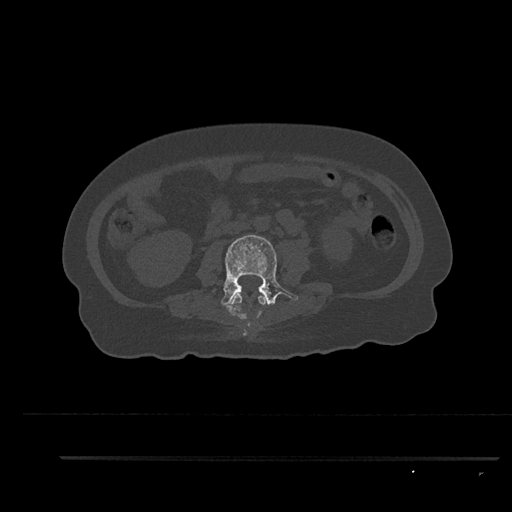
CT including the spine, one axial slice. Position 104 of 797 along the scan axis. Reconstruction kernel Br40s/3. 120 kVp. Bone window (W 1800 / L 400 HU). 0.5 mm slice thickness. 512 × 512 image matrix. Female patient, age 44 years. Case-level facts recorded for this patient, not image findings: primary cancer: renal; vertebrae with lytic lesions (as recorded): L1.
Outlined on this slice (semi-automatically segmented with operator editing):
- L2 vertebra: bounding box (x1, y1, x2, y2) in pixels: (231, 293, 266, 327)
- L3 vertebra: (209, 235, 298, 313)